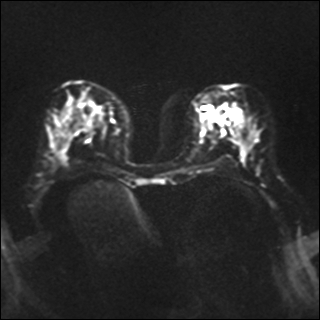
Breast MRI, one axial slice; position 14 of 35 along the scan axis; diffusion-weighted series; image 2 of 4 stored at this slice position (different b-values; order by instance number); 1.5 T; 4 mm slice thickness; 320 × 320 image matrix. Female patient.
Annotated regions visible in this slice (expert manual segmentation):
- tumour on diffusion-weighted imaging: bounding box (x1, y1, x2, y2) in pixels: (212, 106, 230, 123)